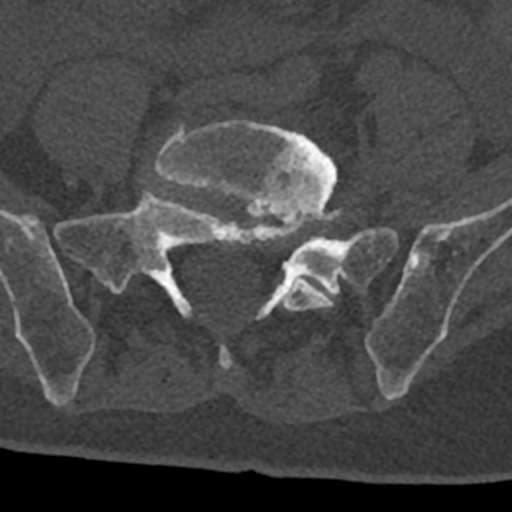
CT including the spine, one axial slice; slice 172 of 797 in the series (ordered by position); reconstruction kernel Br40s/3; bone window (W 1800 / L 400 HU); 0.5 mm slice thickness; 512 × 512 image matrix. Patient: male, 74 years. Case-level facts recorded for this patient, not image findings: primary cancer: renal.
Structures marked on this image (semi-automatic segmentation, software-assisted and operator-edited):
- L5 vertebra: bounding box (x1, y1, x2, y2) in pixels: (154, 120, 337, 370)